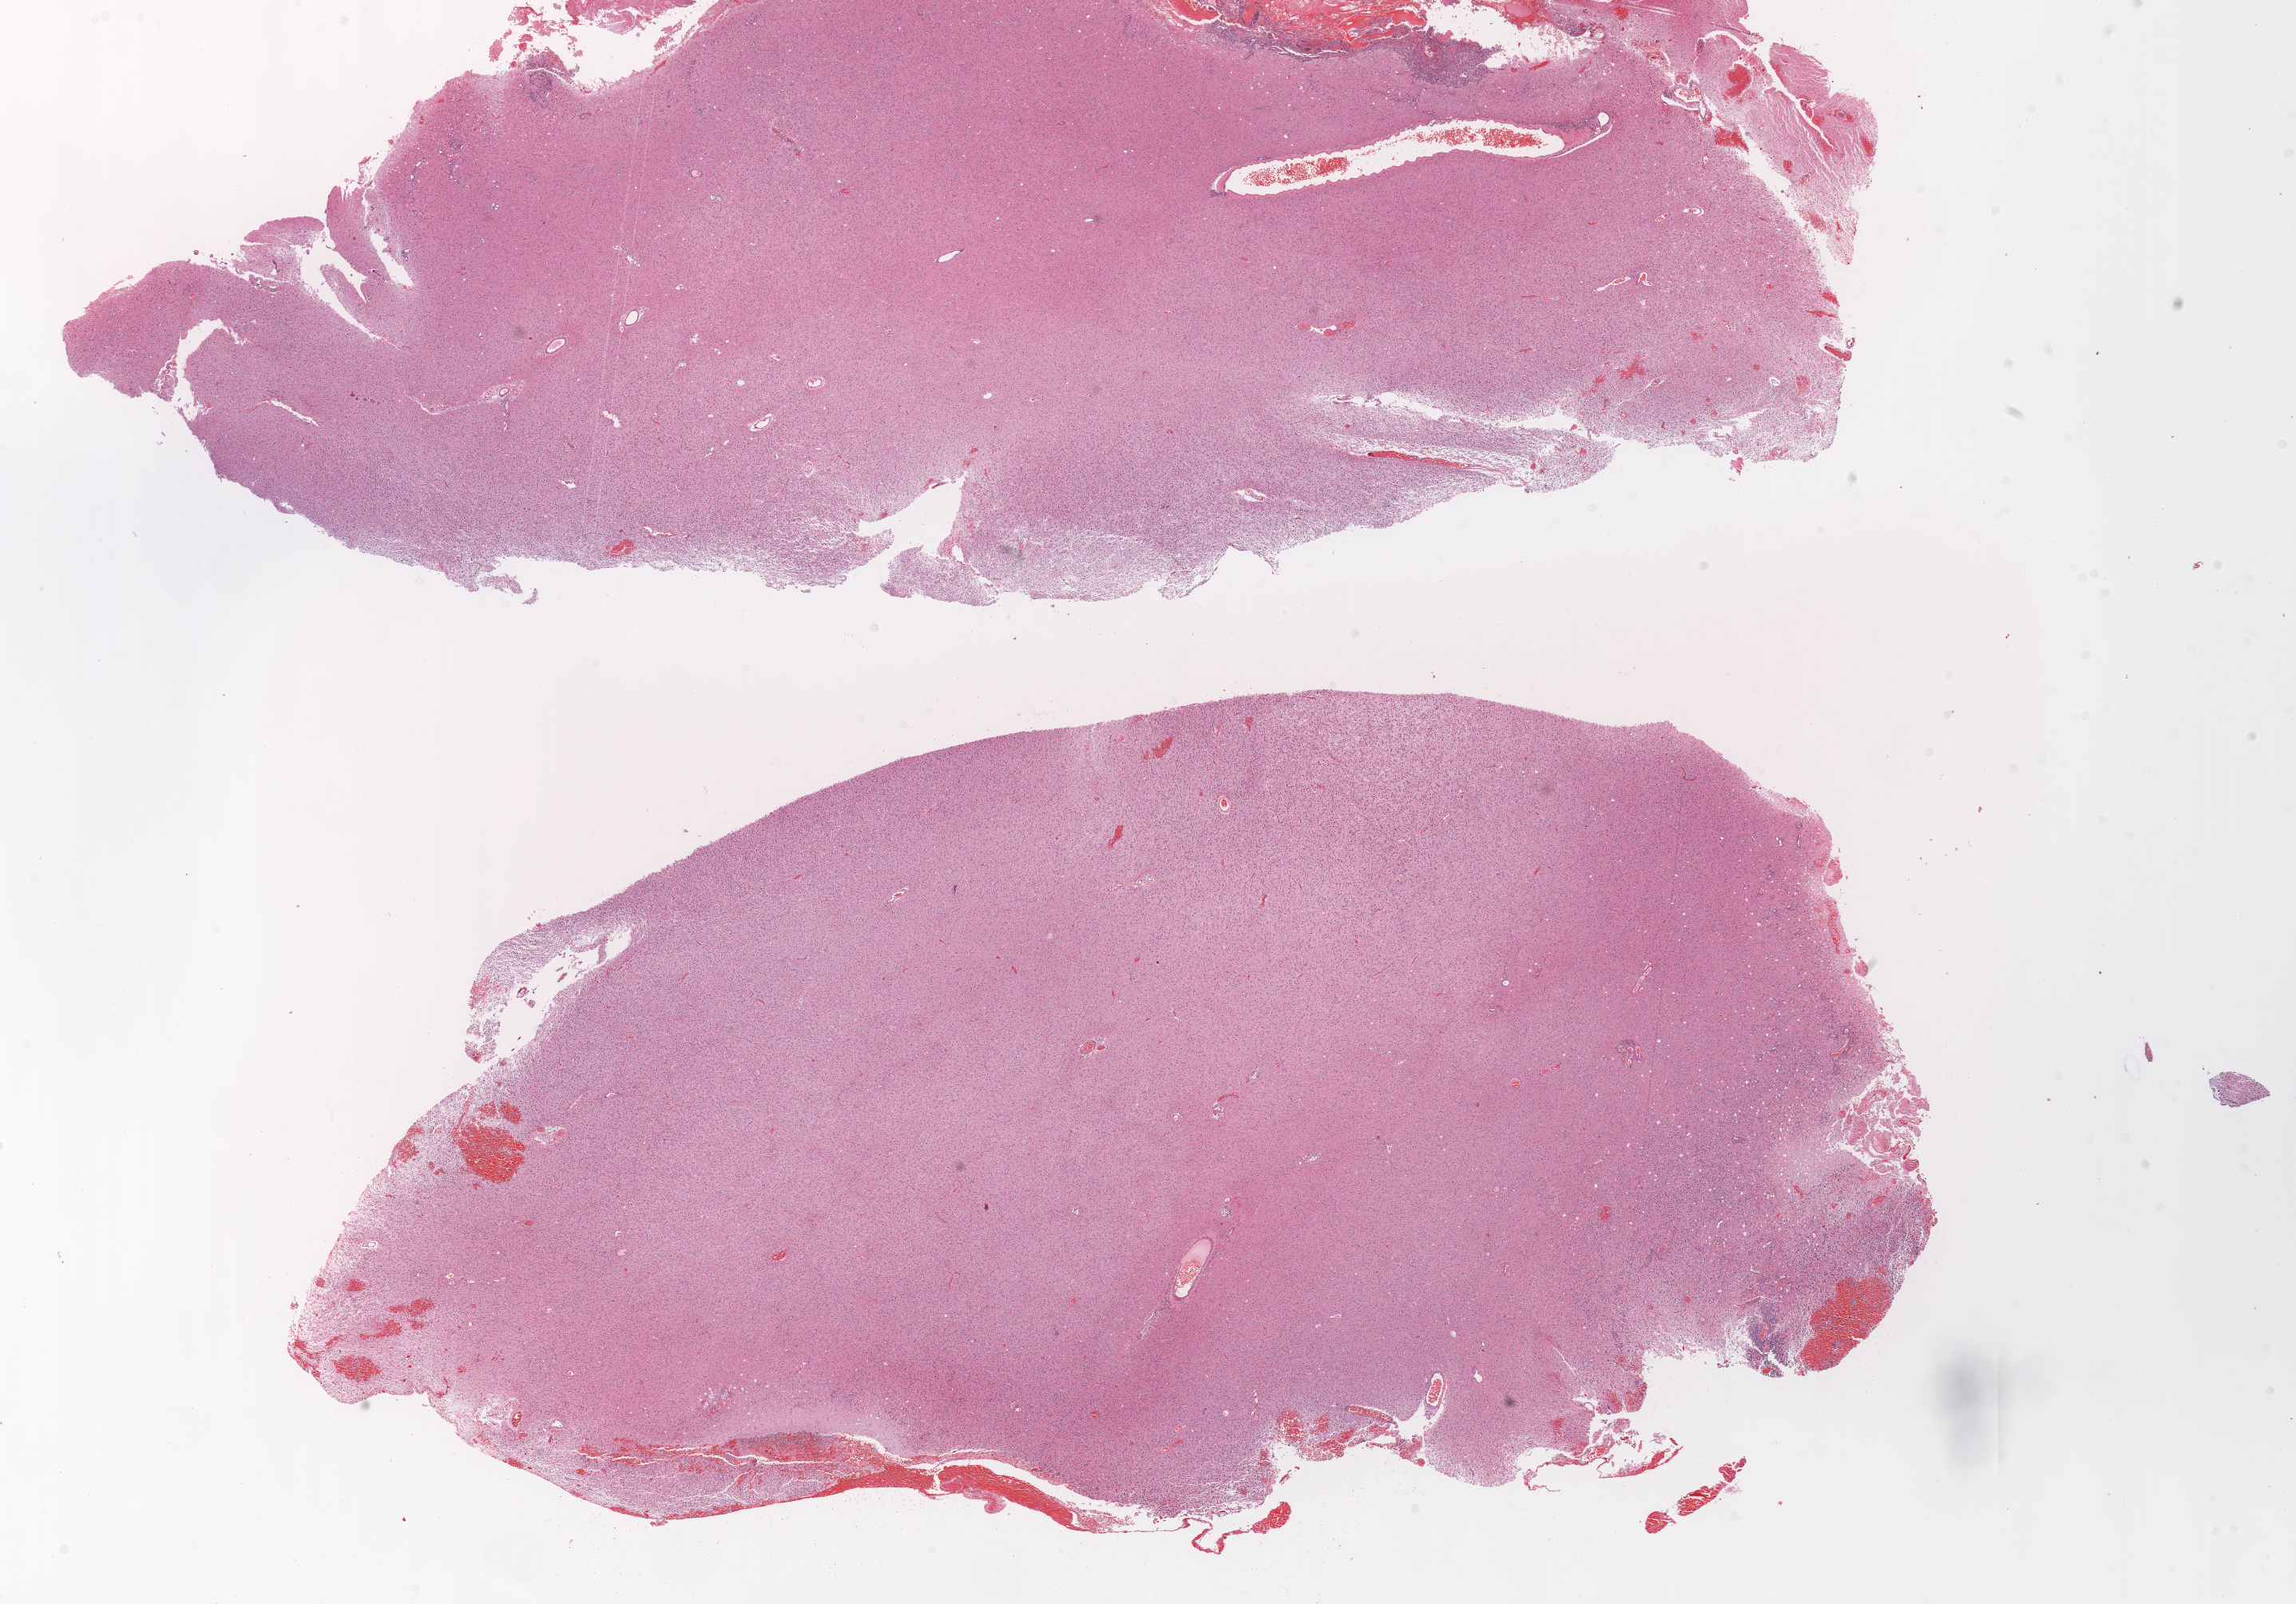
Whole-slide histology image, Hematoxylin and eosin (H&E) stained — low-resolution overview of the scanned area, about 23.1 x 16.1 mm (from a 20x scan), FFPE section, primary tumour sample from the brain. Male, age 38 years at initial diagnosis.
* pathologic diagnosis: Glioblastoma